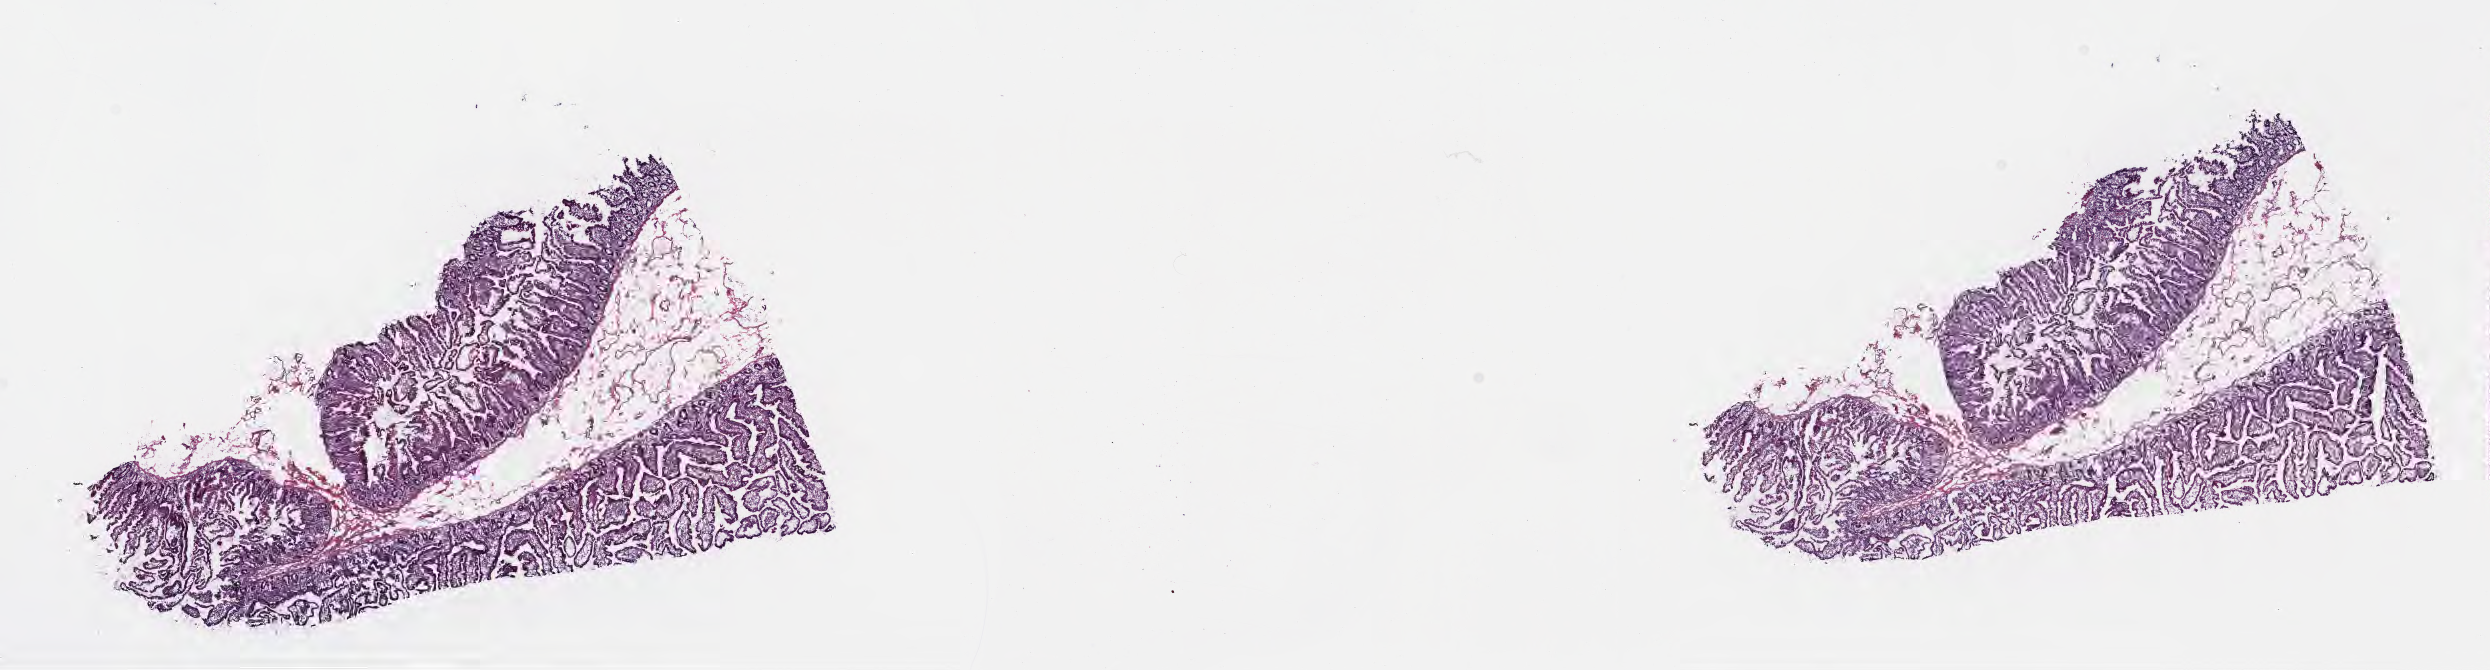
Haematoxylin and eosin whole-slide image — low-resolution overview of the scanned area, about 20.1 x 5.4 mm, cryosection, normal-tissue sample (non-tumor) from a patient with infiltrating duct carcinoma, NOS, site: head of pancreas. Male patient; age at initial diagnosis 57 years.
This section: non-tumor tissue sample; the patient's diagnosis is given above. Section: top of the tissue portion.